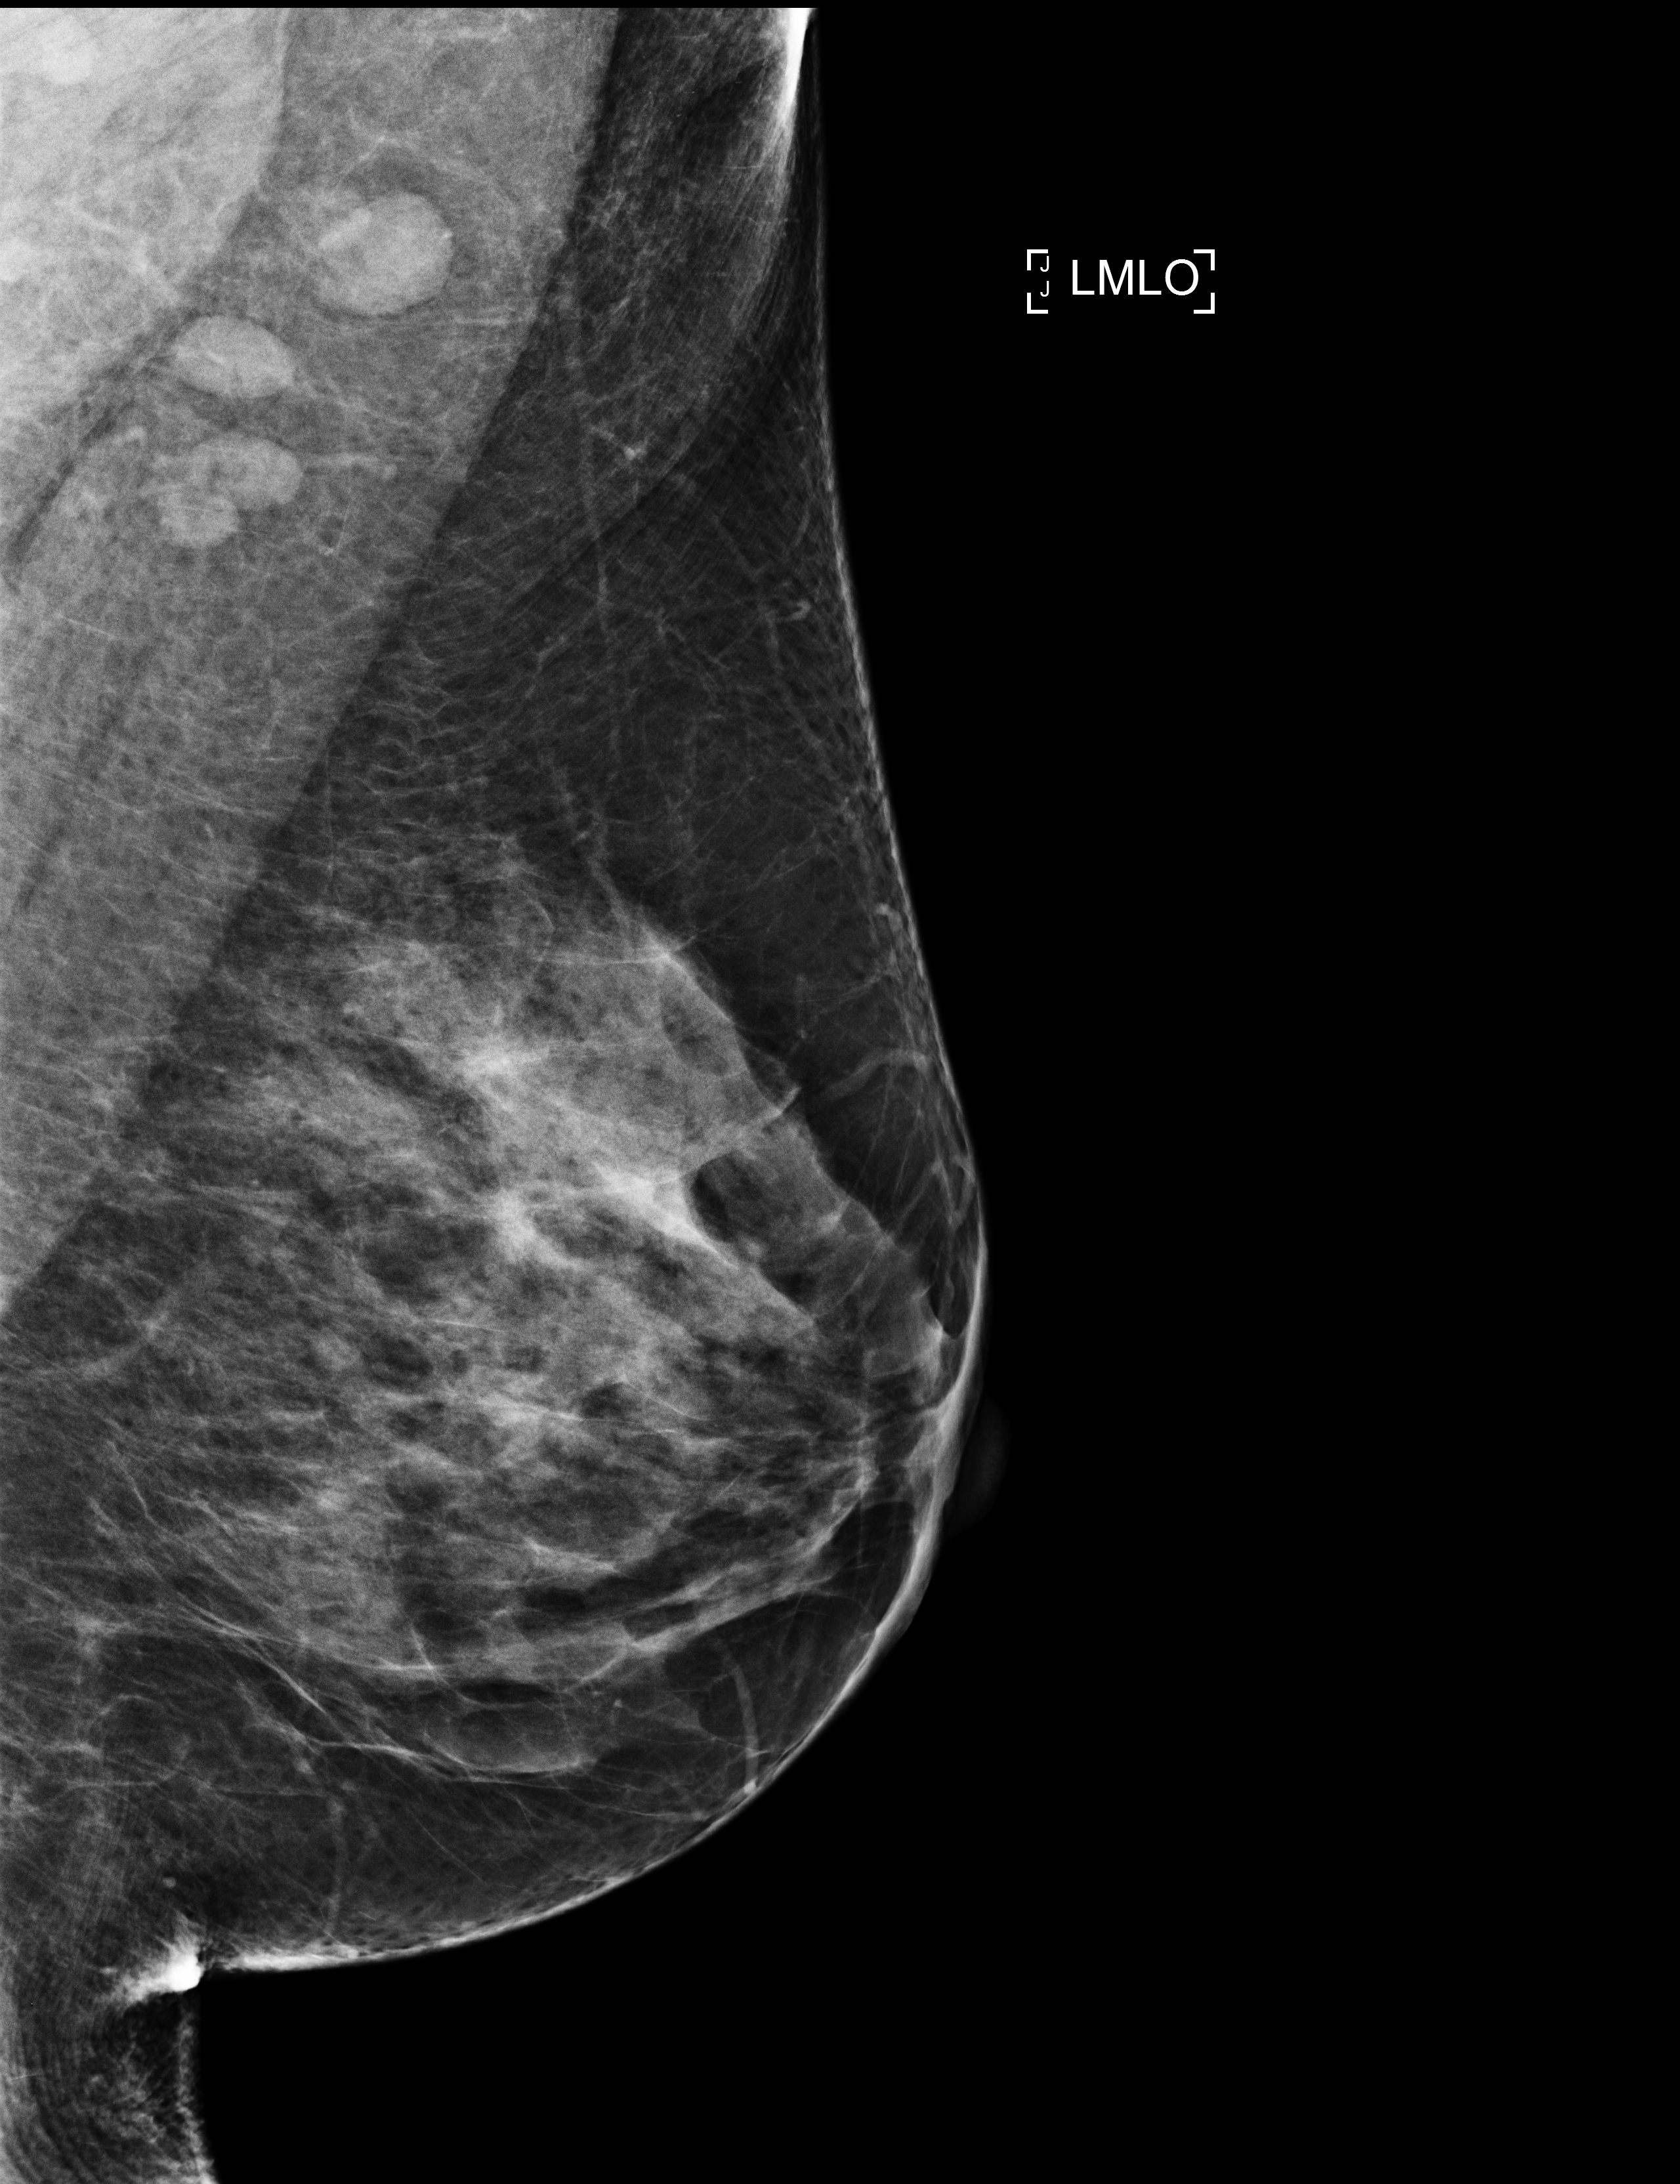
Full-field digital mammogram (FFDM), left breast, mediolateral oblique (MLO) view, annual screening mammography examination, system: Selenia Dimensions. Female patient, age 66 years.
BI-RADS breast density category at the screening exam (both breasts, scale 1–4): 3. Final BI-RADS assessment for this screening round (tomosynthesis exam, both breasts): category 2. Recall: no recall after this screen.